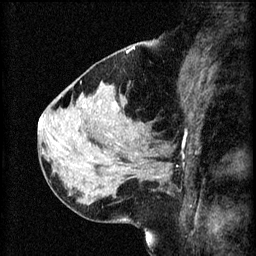
Breast MRI (dynamic contrast-enhanced), one sagittal slice; 3 images stored at this slice position (order not interpretable as contrast timing); 1.5 T; TE 4.2 ms, TR 8.2 ms; 2 mm slice thickness; 256 × 256 image matrix. Female patient, age 37 years.
Structures marked on this image (semi-automatically segmented with operator editing):
- analysis volume of interest (the breast-tissue region the enhancement analysis was run in; not a lesion): bounding box [x1, y1, x2, y2] px = [124, 138, 190, 193]
- tumour enhancement mask (voxels above the 70 % enhancement threshold inside the analysis volume of interest): [154, 138, 186, 177]